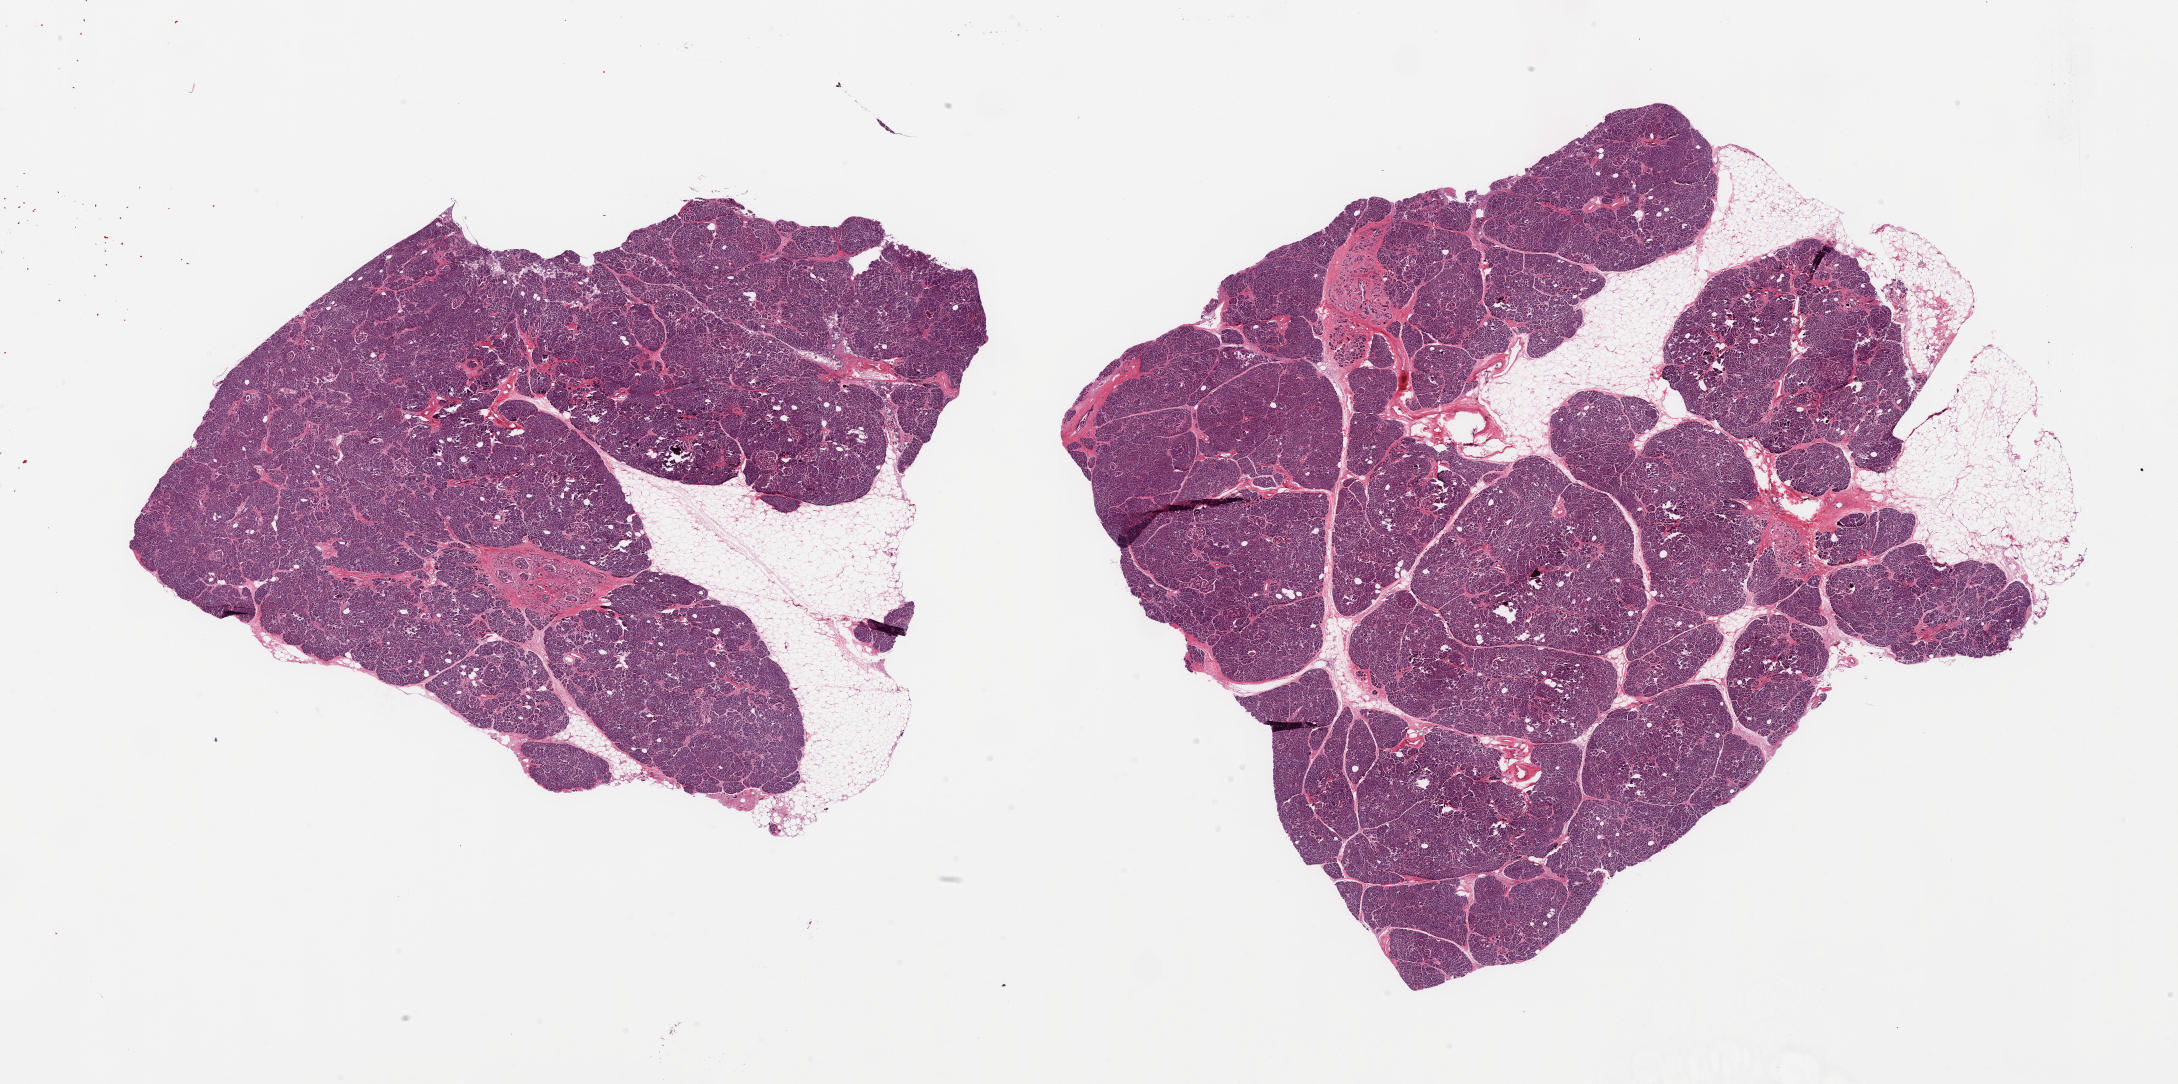
Digitized haematoxylin and eosin-stained section, brightfield, a low-resolution overview of the entire scanned area, about 34.5 x 17.1 mm. PAXgene-fixed, paraffin-embedded tissue. Sampled site (target tissue): pancreas. Donor tissue sample. Male donor.
- reviewer comment on this tissue sample: 2 pieces; both include mostly attached fat up to ~20%, some intralobular fibrosis and circumscribed area of atrophy, fibrosis, and mucinous metaplpasia of small duct branches